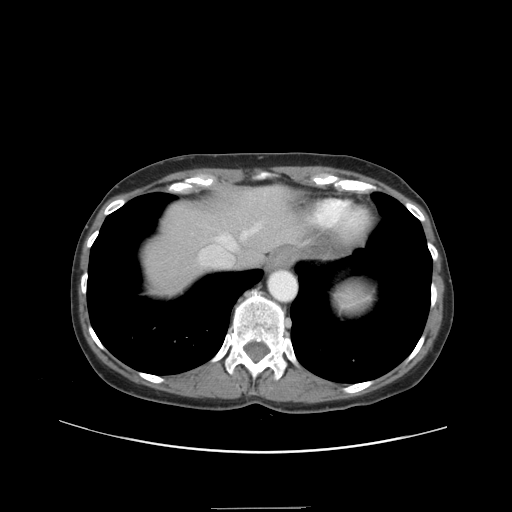
Contrast-enhanced abdominal CT, one axial slice. Position 33 of 38 along the scan axis. Reconstruction kernel STANDARD. 120 kVp. Intravenous contrast given. Soft-tissue window (W 400 / L 40 HU). 5 mm slice thickness. 512 × 512 image matrix, field of view 388 × 388 mm. Female patient, age 64 years. Case-level facts recorded for this patient, not image findings: diagnosis: colorectal cancer liver metastases, imaged before liver resection; multiple liver metastases: no; largest metastasis: 3.8 cm; chemotherapy before resection: yes.
Outlined on this slice (manually delineated by an expert):
- hepatic veins: bounding box [x1, y1, x2, y2] px = [200, 223, 260, 266]
- liver: [142, 191, 299, 290]
- planned liver remnant (the part of the liver to remain after resection): [171, 191, 299, 265]